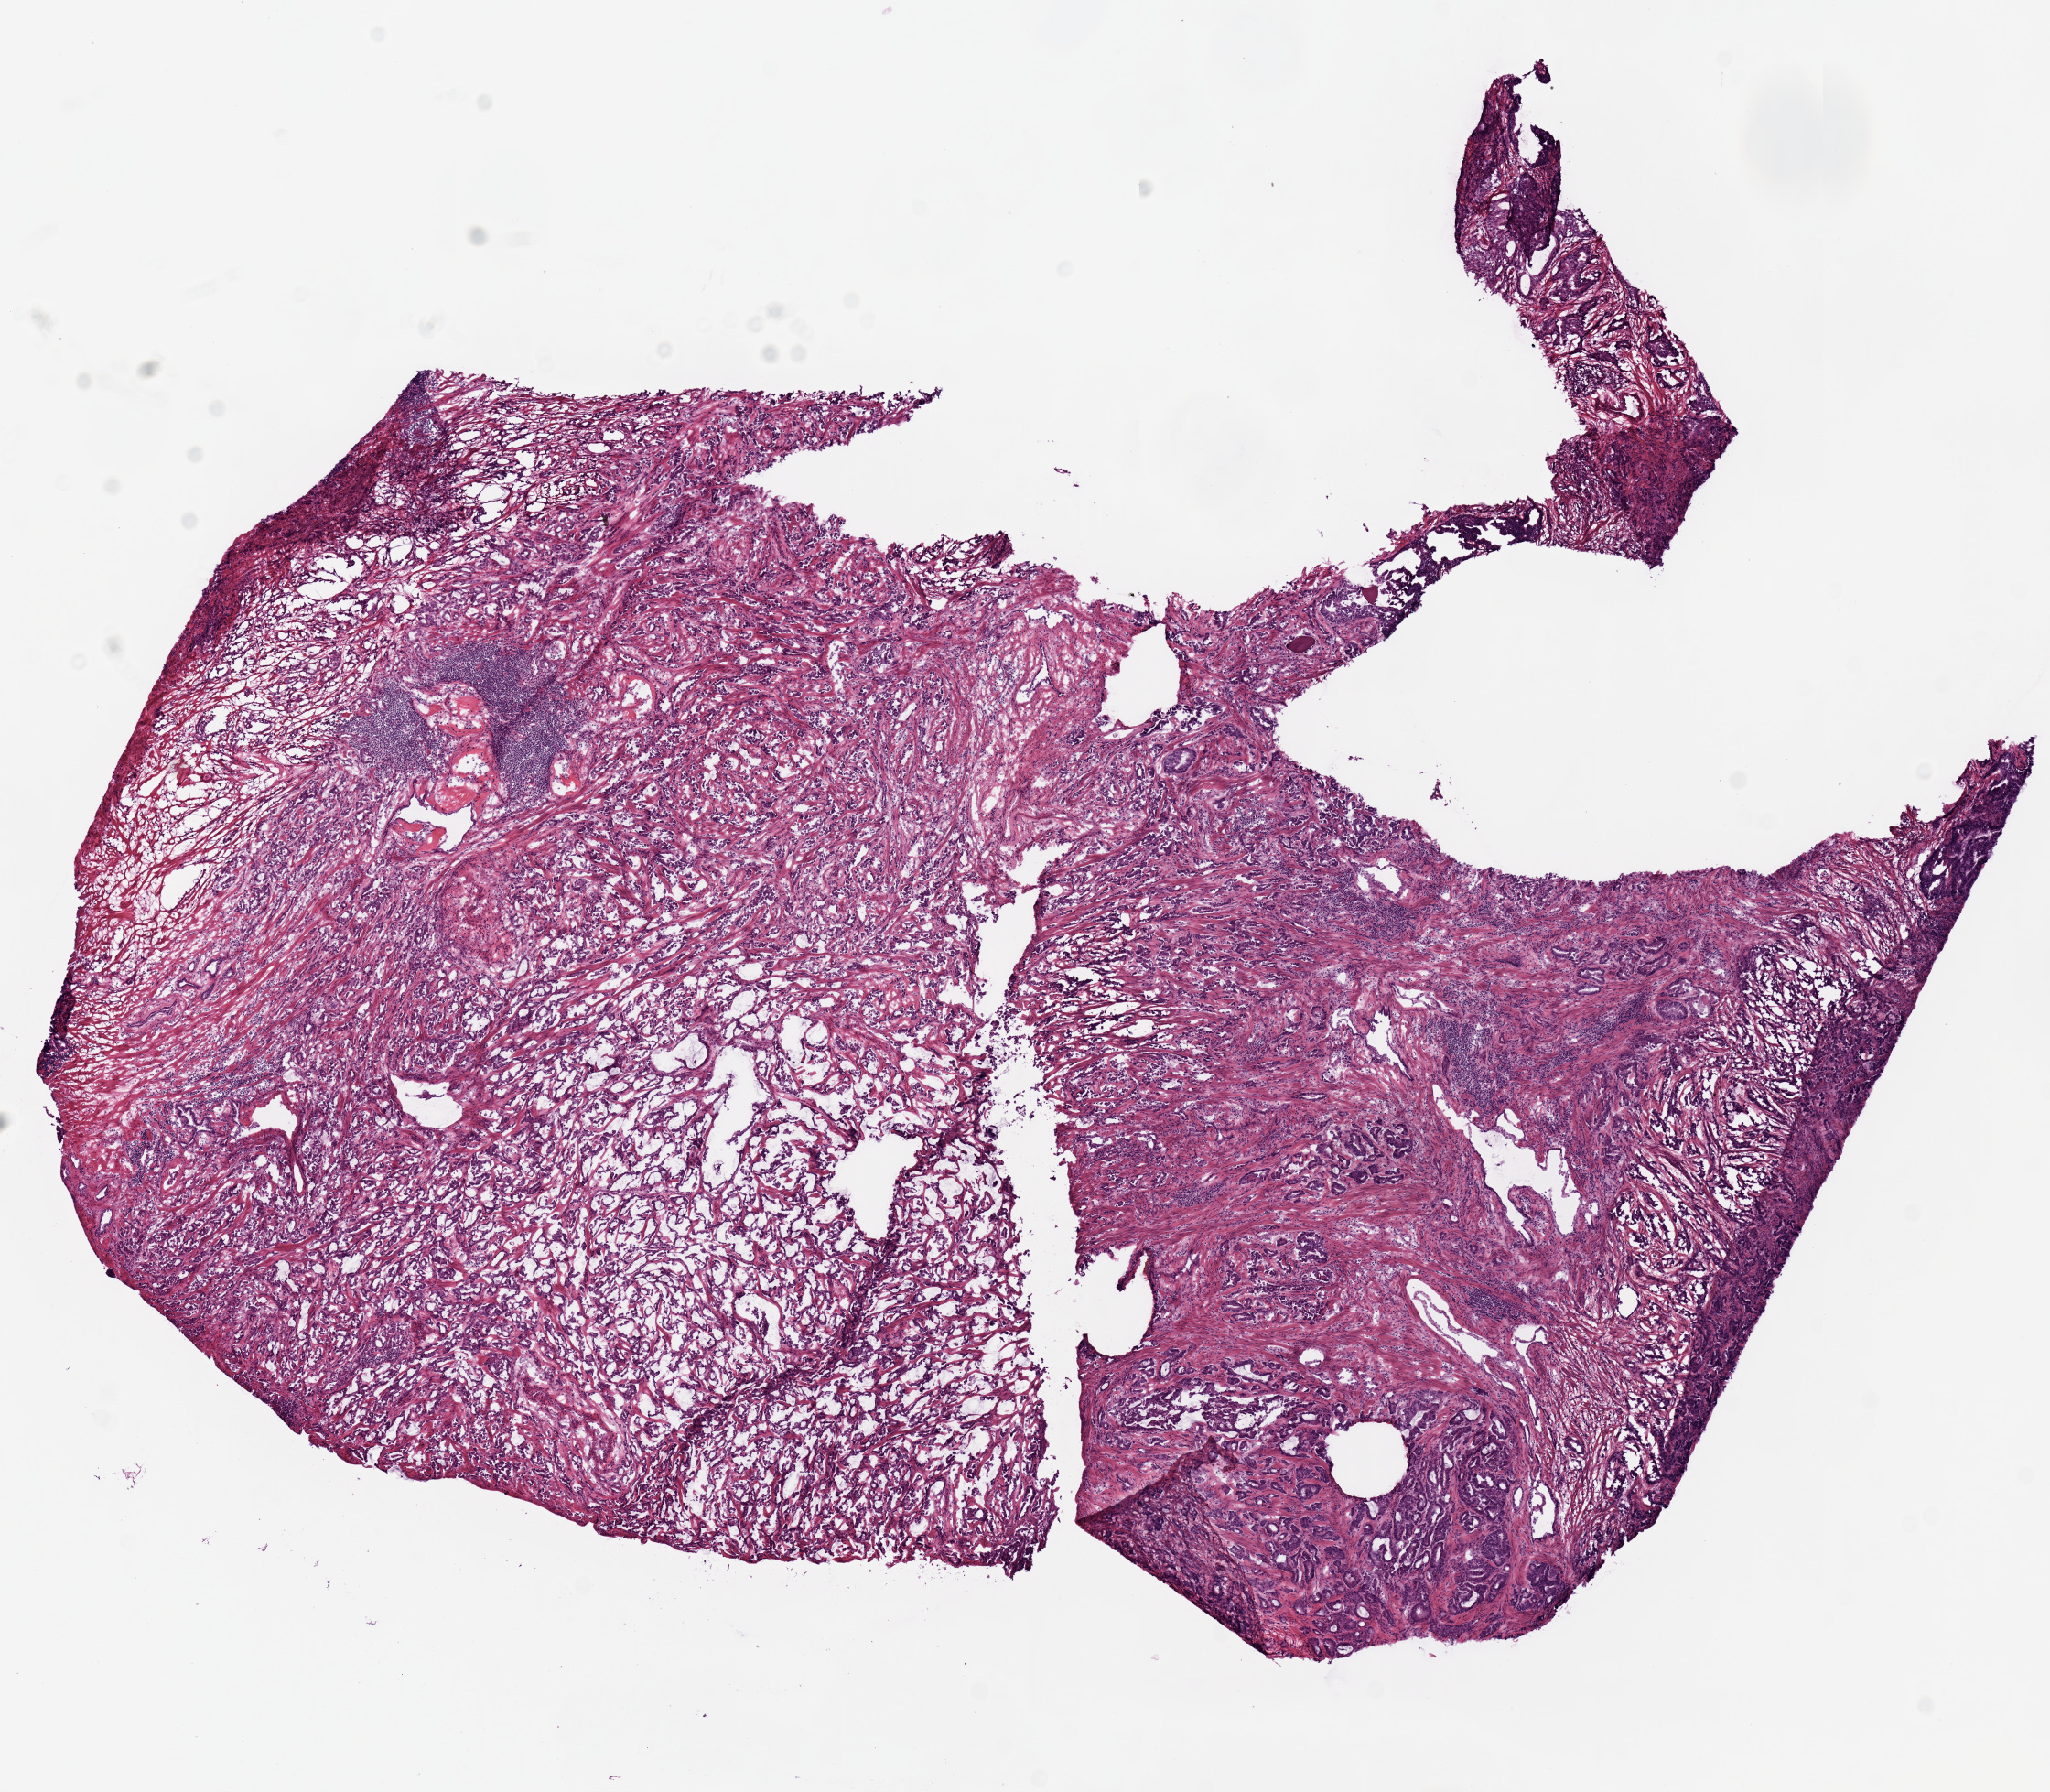
Hematoxylin and eosin (H&E) stained whole-slide image — low-resolution overview of the scanned area, about 8.9 x 7.7 mm, frozen section, sample: primary tumour, prostate. Male patient; age at initial diagnosis 68 years. Gleason score: 7 (4+3). Composition of this section per pathologist review: tumour nuclei 75%, necrosis 0%.
Histologic diagnosis: Acinar cell carcinoma (prostate gland). Lymph nodes positive (case pathology): 0 of 7 examined.